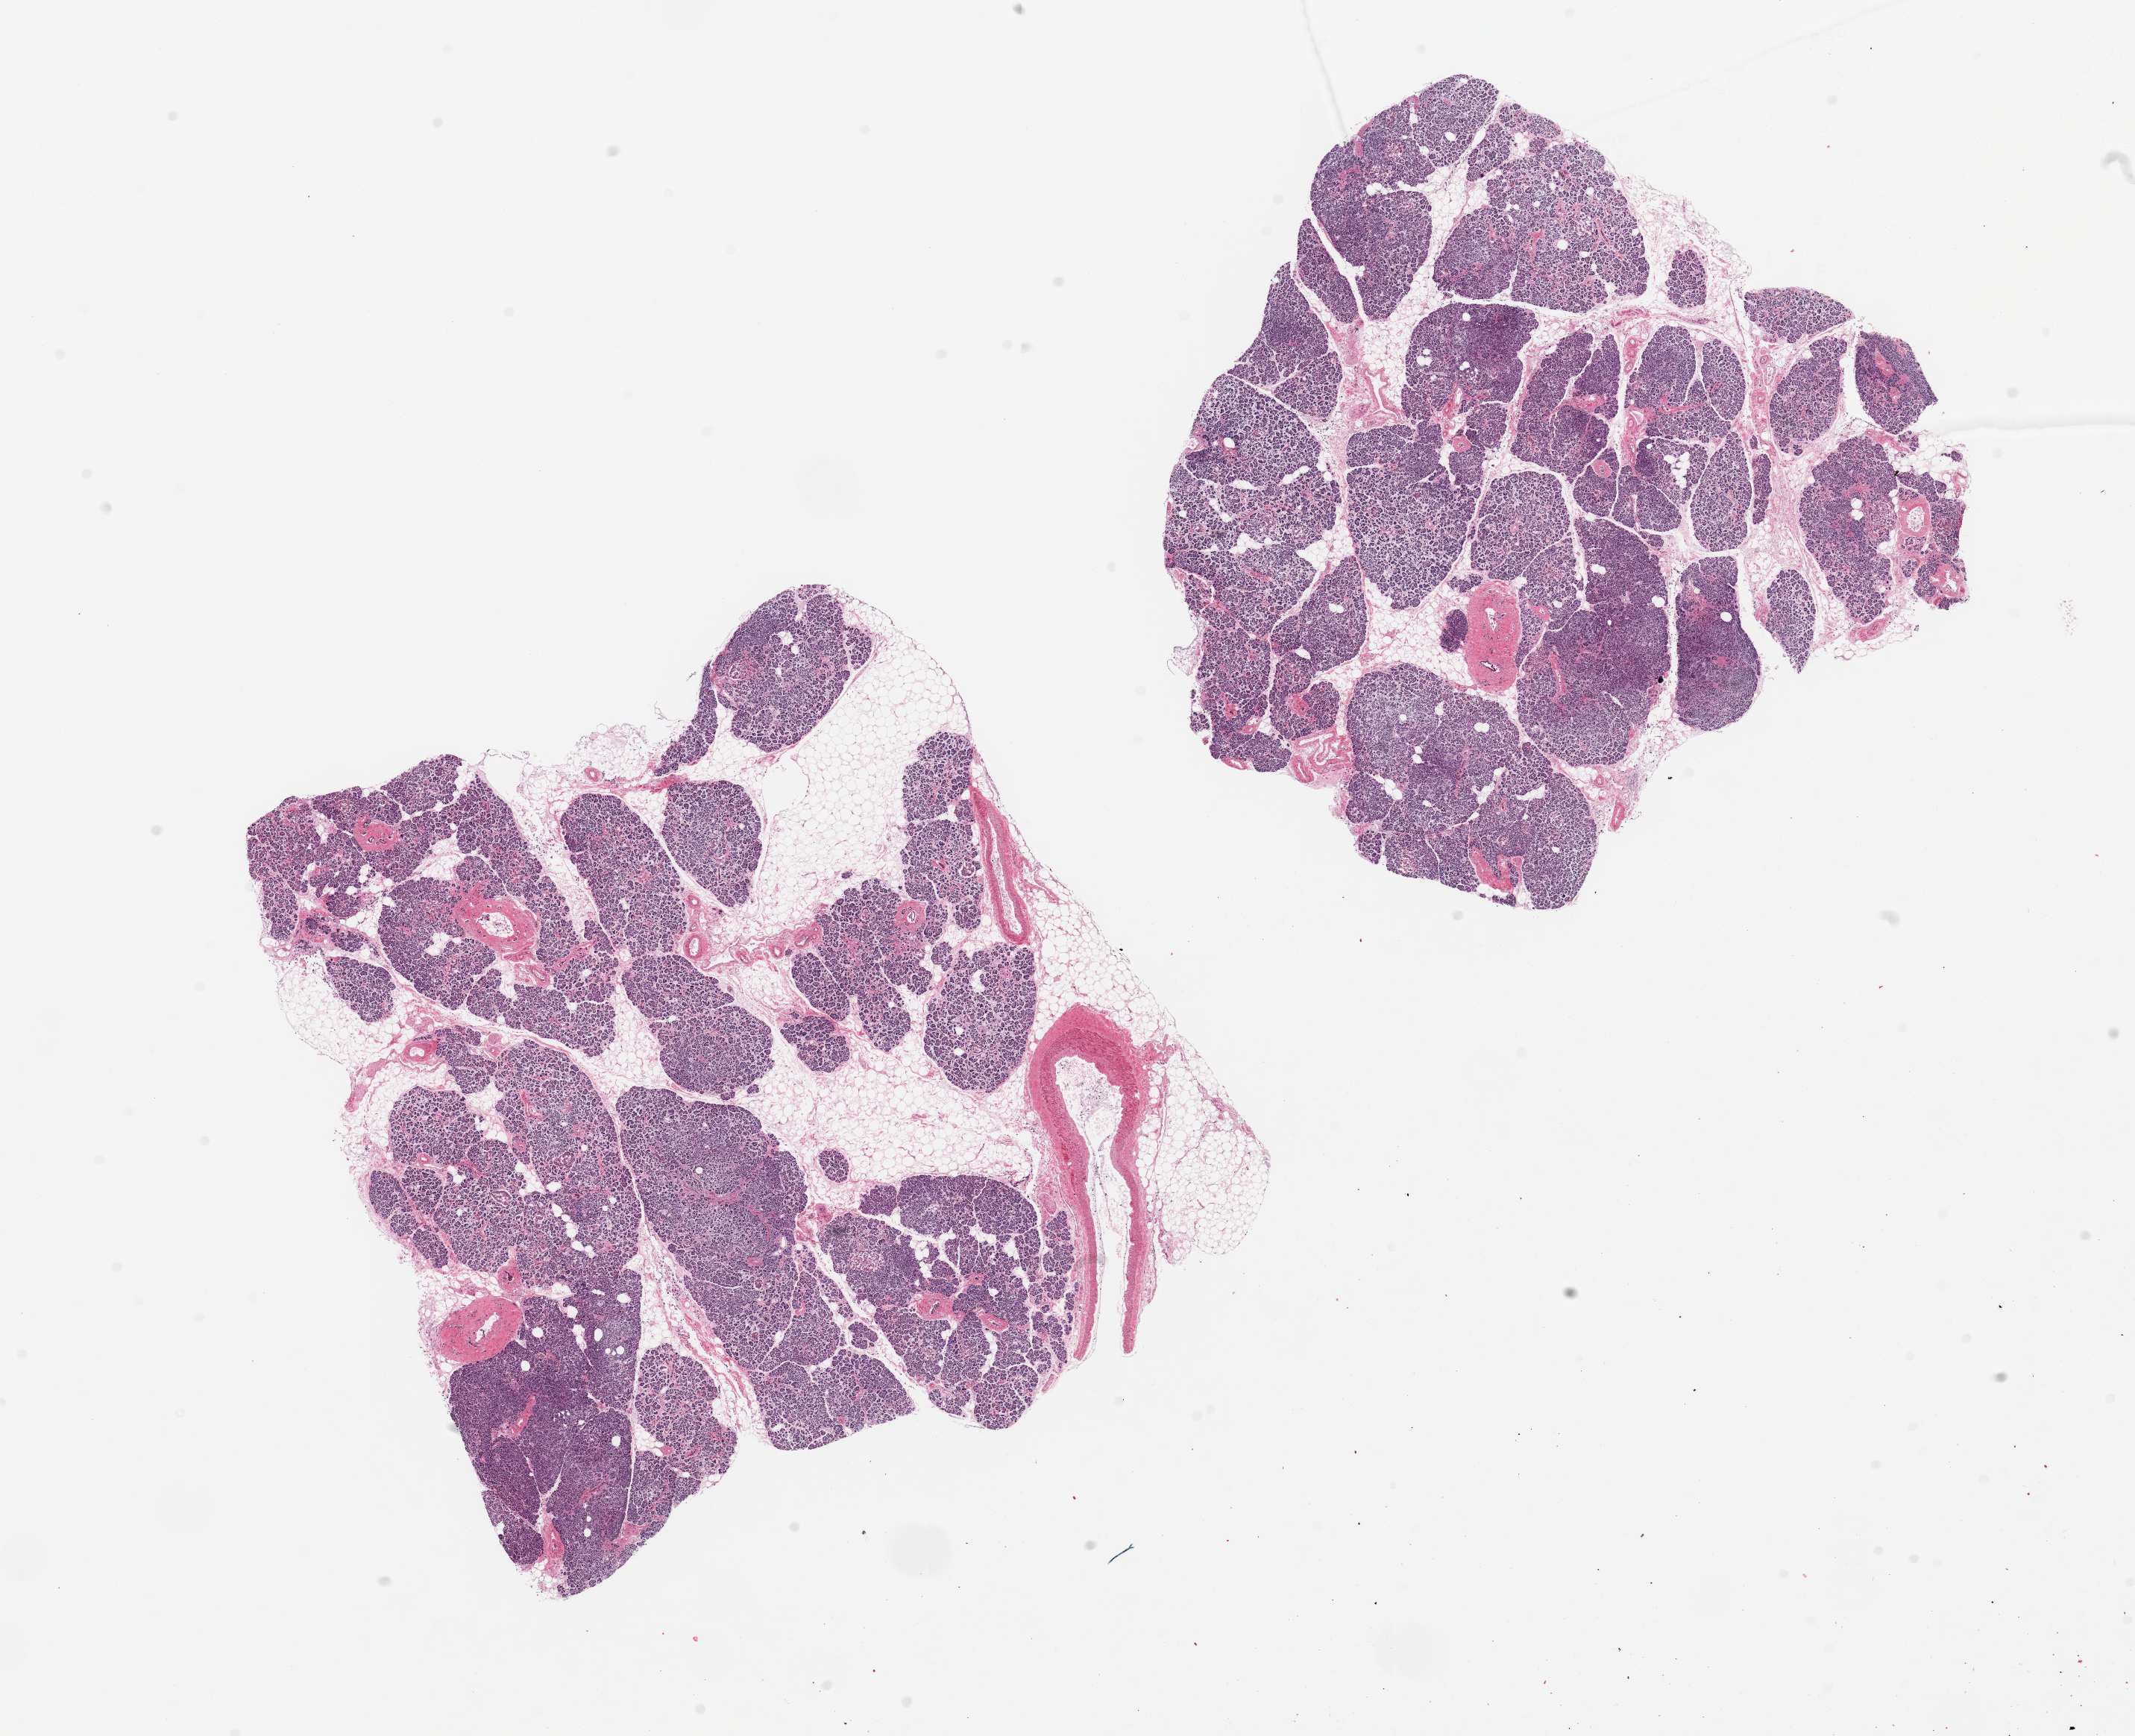
Hematoxylin and eosin (H&E) whole-slide image — whole scanned area (about 22.6 x 18.4 mm, from a 20x scan) shown as a low-resolution overview. PAXgene-fixed paraffin-embedded (PFPE) section. Sampled site (target tissue): pancreas. Tissue donor sample. Donor: female.
- pathologist's review note for this sample: 2 pieces; 30 & 20% internal fat